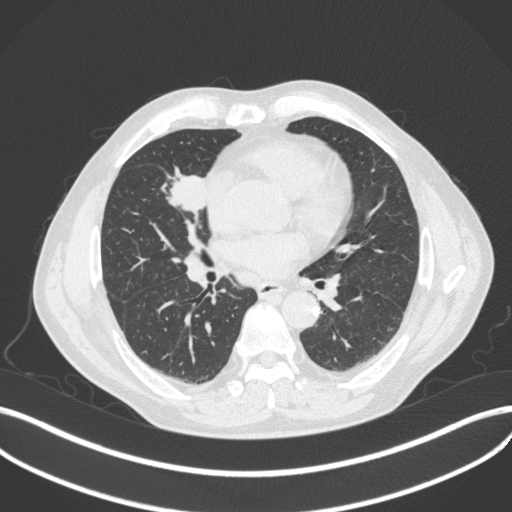
Chest CT, one axial slice. Slice 195 of 429 in the series (ordered by position). Reconstruction kernel B31f. Lung window (W 1500 / L -600 HU). 1 mm slice thickness. 512 × 512 image matrix, field of view 400 × 400 mm. Male patient, age 61 years. Case-level facts recorded for this patient, not image findings: clinical TNM (as recorded): T2b N1 M0.
Annotated regions visible in this slice (bounding box drawn by a radiologist):
- lung tumour (recorded histology: squamous cell carcinoma): bounding box (x1, y1, x2, y2) in pixels: (164, 168, 212, 228)